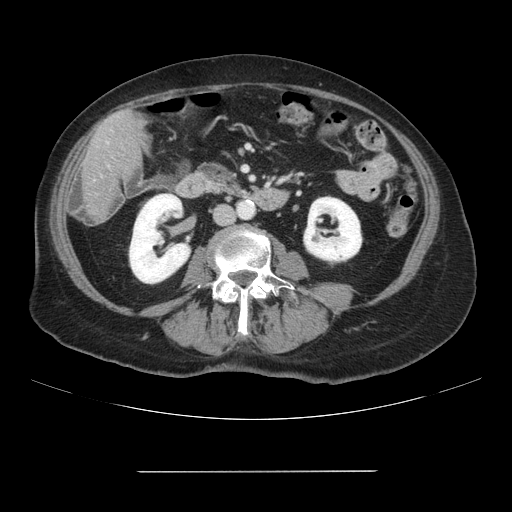
Contrast-enhanced abdominal CT, one axial slice; 120 kVp; intravenous contrast given; soft-tissue window (W 400 / L 40 HU); 512 × 512 image matrix, field of view 400 × 400 mm. Female patient, age 74 years. From the clinical record (not read from this slice): diagnosis: colorectal cancer liver metastases, imaged before liver resection; multiple liver metastases: yes.
Annotated regions visible in this slice (expert manual segmentation):
- liver: box from (x=83, y=111) to (x=143, y=221) px